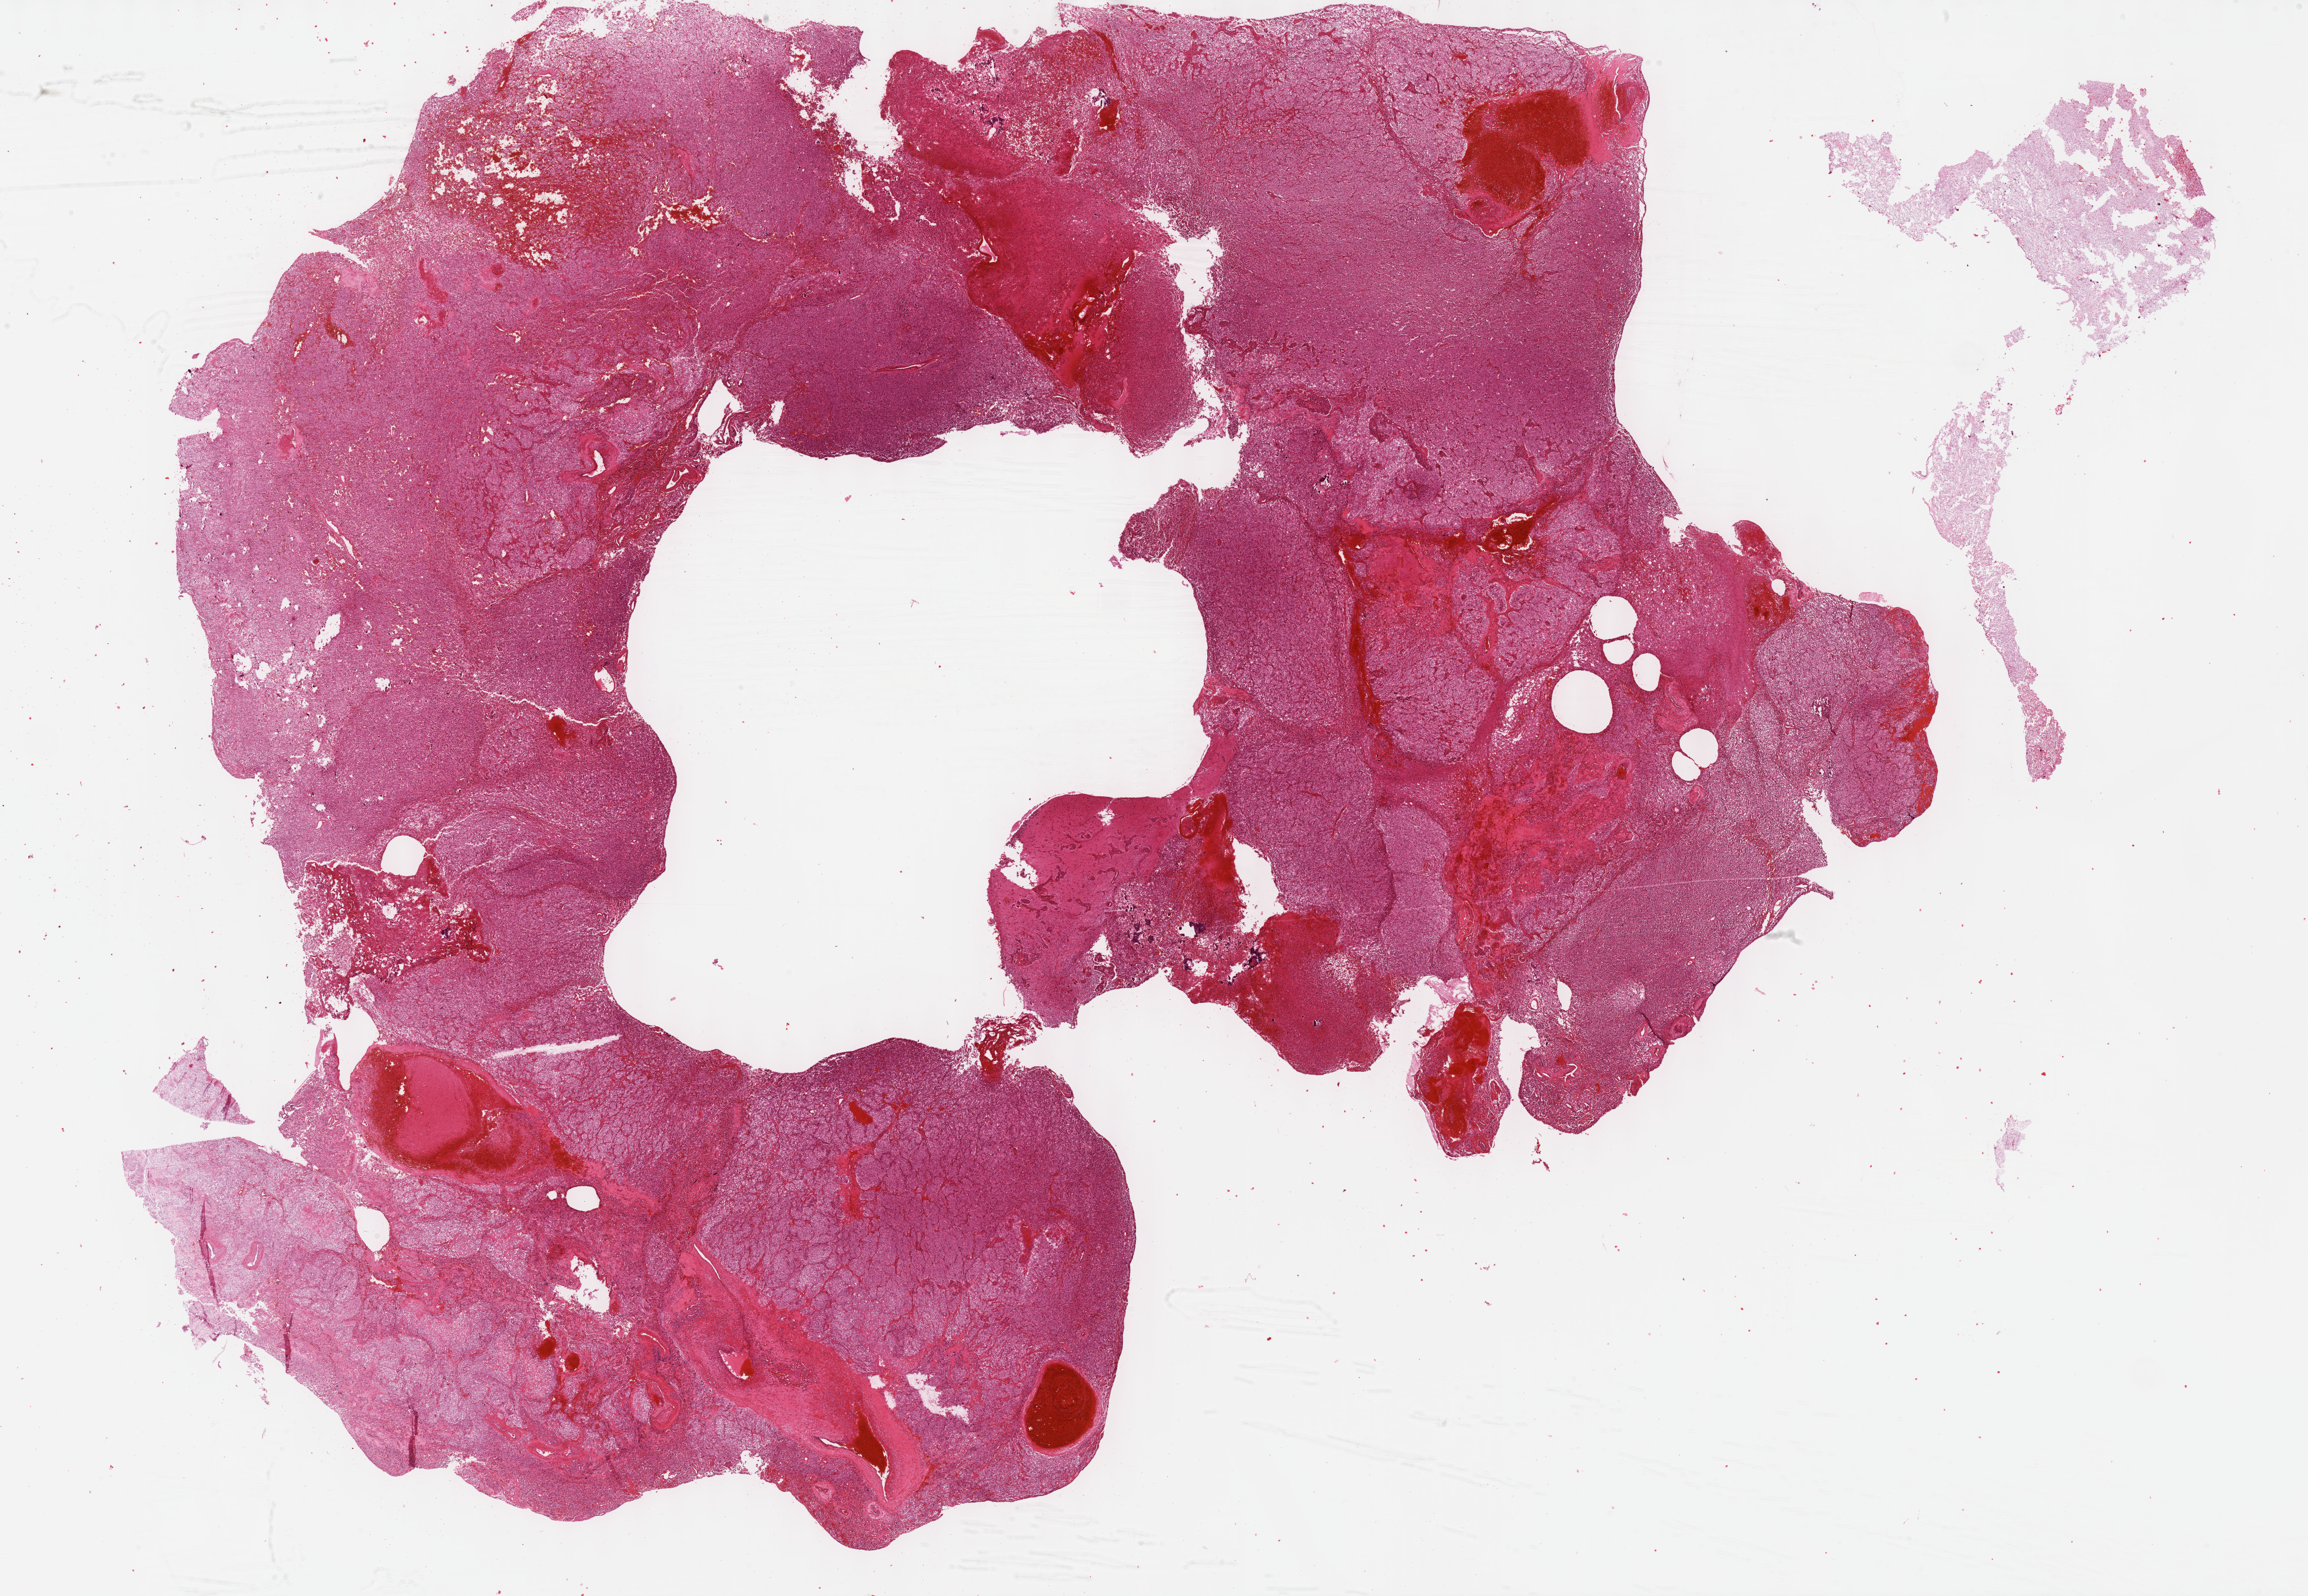
H&E whole-slide image — whole scanned area (about 31.7 x 21.9 mm, from a 40x scan) shown as a low-resolution overview, formalin-fixed paraffin-embedded (FFPE) diagnostic section, brain, primary tumour sample. Male, age 40 years at initial diagnosis. Histologic grade: G3 (poorly differentiated).
- pathologic diagnosis: Oligodendroglioma, anaplastic (cerebrum)
- laterality: left